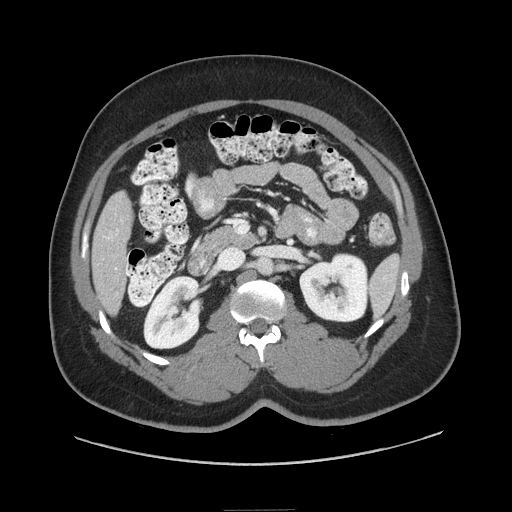
Contrast-enhanced abdominal CT (liver protocol), one axial slice; slice 24 of 87 in the series (ordered by position); reconstruction kernel STANDARD; soft-tissue window (W 400 / L 40 HU); 2.5 mm slice thickness; 512 × 512 image matrix, field of view 440 × 440 mm. Case-level facts recorded for this patient, not image findings: diagnosis: hepatocellular carcinoma (patient treated with transarterial chemoembolisation; whether this scan precedes or follows treatment is not stated here); TNM stage (as recorded): Stage-II; Child-Pugh class: A.
Outlined on this slice (semi-automatic segmentation, software-assisted and operator-edited):
- liver parenchyma outside the tumour (the mass and vessels are separate outlines, so this box may not span the whole liver): bounding box (x1, y1, x2, y2) in pixels: (92, 190, 132, 314)
- liver vessels: (106, 229, 118, 239)